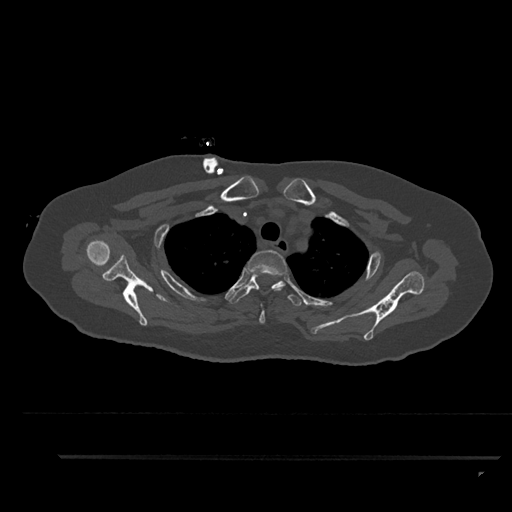
CT including the spine, one axial slice. Slice 702 of 797 in the series (ordered by position). Reconstruction kernel Br40s/3. 120 kVp. Bone window (W 1800 / L 400 HU). 0.5 mm slice thickness. 512 × 512 image matrix, field of view 408 × 408 mm. Patient: female, 44 years. Case-level facts recorded for this patient, not image findings: primary cancer: renal.
Annotated regions visible in this slice (semi-automatic segmentation, software-assisted and operator-edited):
- T2 vertebra: bounding box <248,250,287,324> (left, top, right, bottom; pixels)
- T3 vertebra: <228,272,304,306>